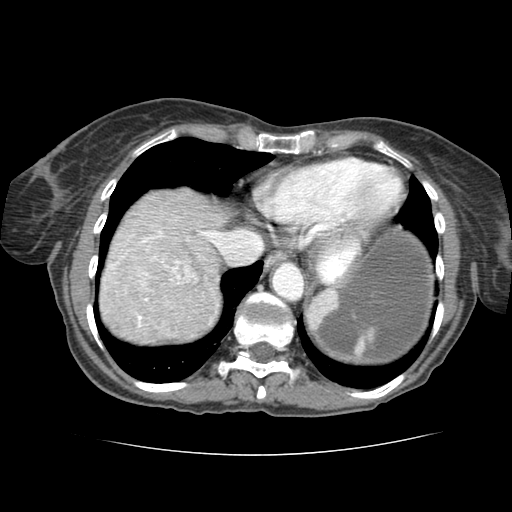
Contrast-enhanced abdominal CT (liver protocol), one axial slice; slice 70 of 77 in the series (ordered by position); reconstruction kernel STANDARD; soft-tissue window (W 400 / L 40 HU); 2.5 mm slice thickness; 512 × 512 image matrix, field of view 340 × 340 mm. Case-level facts recorded for this patient, not image findings: diagnosis: hepatocellular carcinoma (patient treated with transarterial chemoembolisation; whether this scan precedes or follows treatment is not stated here); TNM stage (as recorded): Stage-I.
Outlined on this slice (semi-automatically segmented with operator editing):
- abdominal aorta: bounding box <272,263,304,300> (left, top, right, bottom; pixels)
- liver parenchyma outside the tumour (the mass and vessels are separate outlines, so this box may not span the whole liver): <104,192,234,330>
- mass: <165,286,202,321>
- liver vessels: <185,281,205,318>